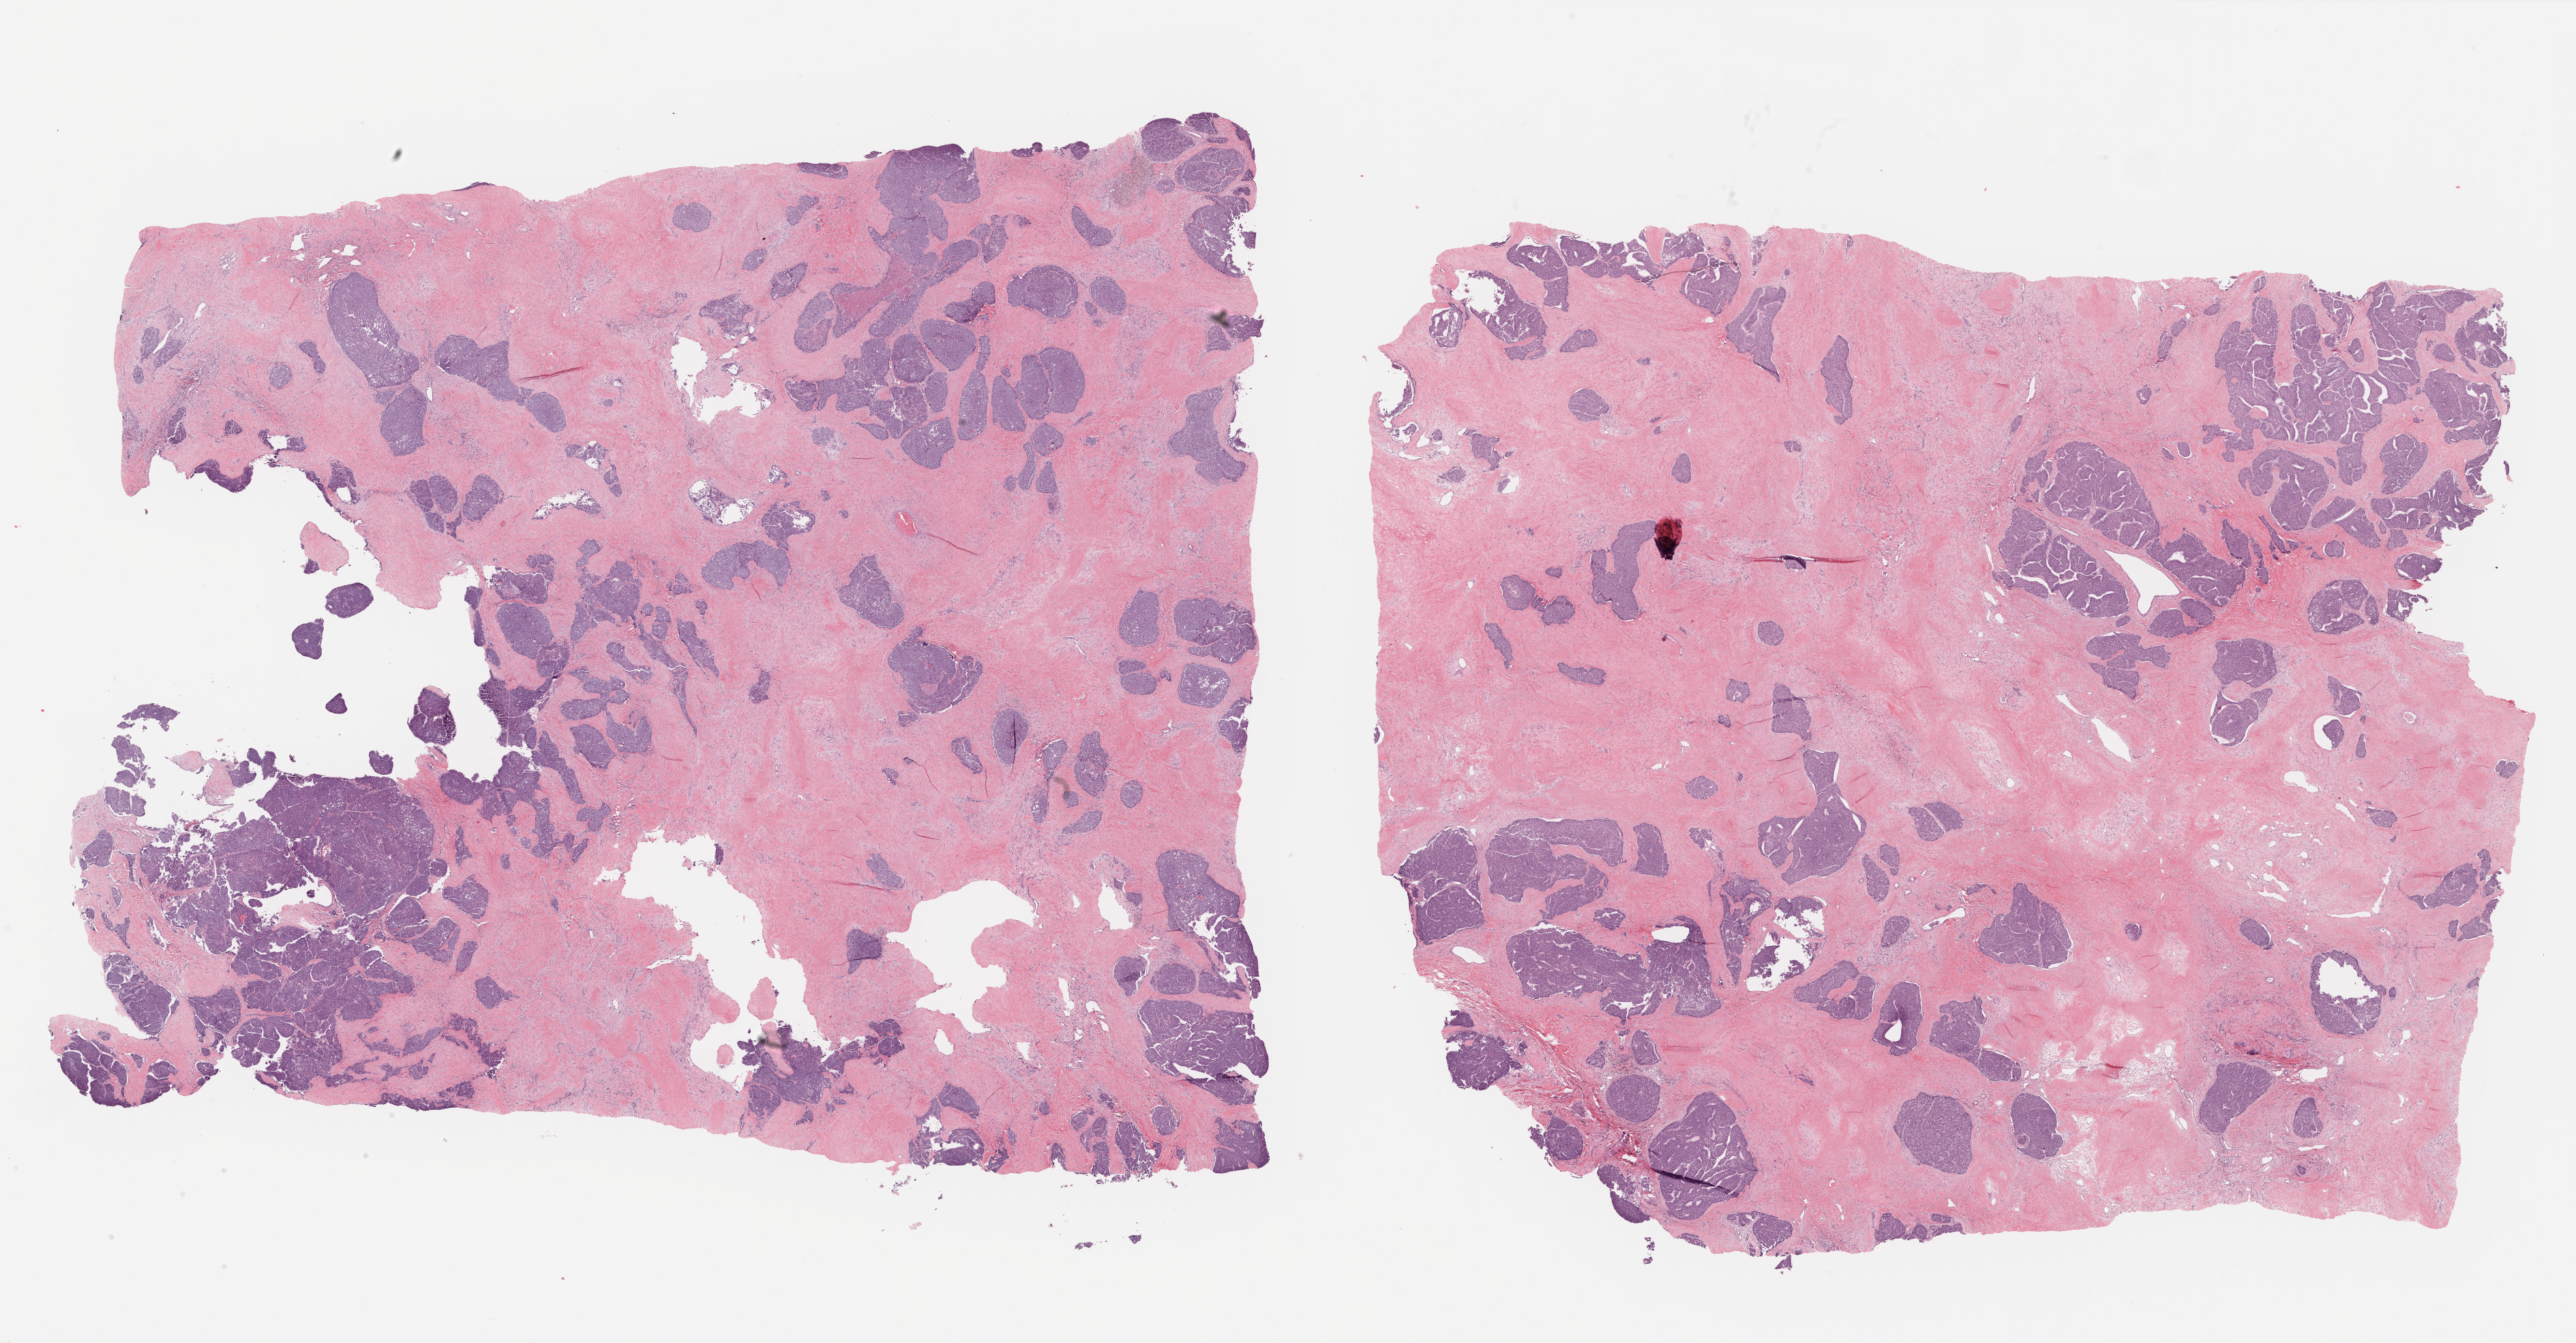
Digitized Hematoxylin and eosin (H&E) stained tissue section (whole slide), low-resolution overview of the scanned area, about 30.6 x 15.9 mm. FFPE section. Liver, primary tumour sample. Male, age 23 years at initial diagnosis. Histologic grade: G3 (poorly differentiated).
* AJCC pathologic stage: III (6th edition)
* pathologic diagnosis: Hepatocellular carcinoma, NOS